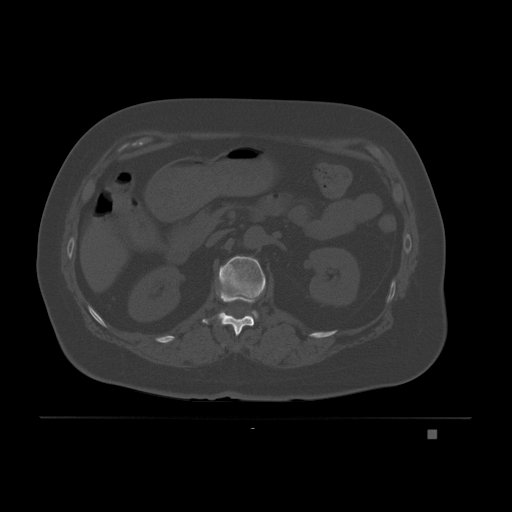
CT including the spine, one axial slice. Position 77 of 221 along the scan axis. Bone window (W 1800 / L 400 HU). 3 mm slice thickness. 512 × 512 image matrix. Patient: female, 63 years. From the clinical record (not read from this slice): primary cancer: breast.
Outlined on this slice (semi-automatic segmentation, software-assisted and operator-edited):
- L1 vertebra: bounding box <218,255,266,322> (left, top, right, bottom; pixels)
- T12 vertebra: <202,290,254,336>